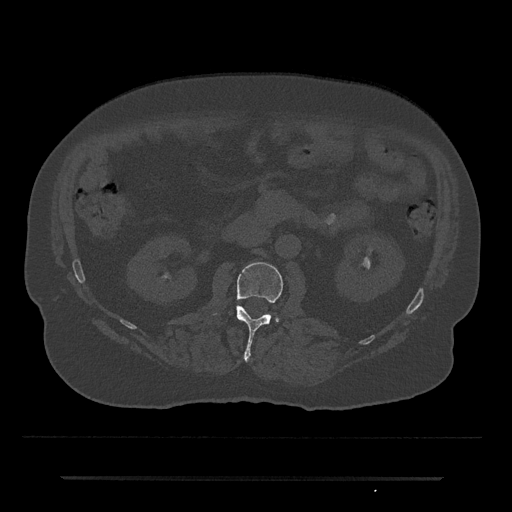
CT including the spine, one axial slice. Slice 5 of 797 in the series (ordered by position). Reconstruction kernel Br40s/3. 120 kVp. Bone window (W 1800 / L 400 HU). 512 × 512 image matrix, field of view 437 × 437 mm. Patient: male, 69 years. Case-level facts recorded for this patient, not image findings: primary cancer: prostate.
Annotated regions visible in this slice (semi-automatic segmentation, software-assisted and operator-edited):
- L2 vertebra: bounding box <213,262,283,361> (left, top, right, bottom; pixels)